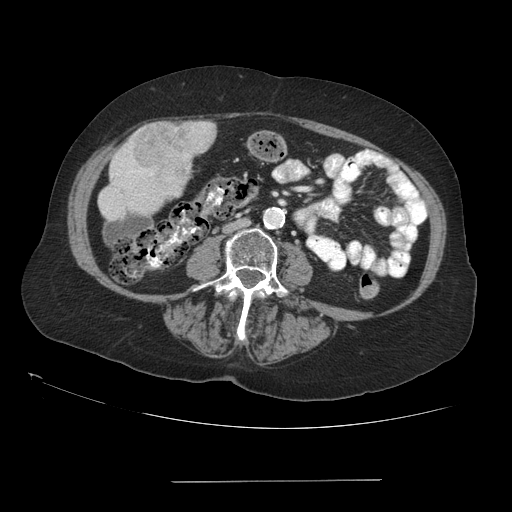
Contrast-enhanced abdominal CT (liver protocol), one axial slice; position 19 of 89 along the scan axis; 140 kVp; soft-tissue window (W 400 / L 40 HU); 2.5 mm slice thickness; 512 × 512 image matrix, field of view 400 × 400 mm. From the clinical record (not read from this slice): diagnosis: hepatocellular carcinoma (patient treated with transarterial chemoembolisation; whether this scan precedes or follows treatment is not stated here); TNM stage (as recorded): Stage-IVA; Child-Pugh class: A; tumour differentiation: poorly differentiated; tumour nodularity: uninodular.
Annotated regions visible in this slice (semi-automatic segmentation, software-assisted and operator-edited):
- liver parenchyma outside the tumour (the mass and vessels are separate outlines, so this box may not span the whole liver): bounding box <98,124,216,222> (left, top, right, bottom; pixels)
- mass: <132,120,217,195>